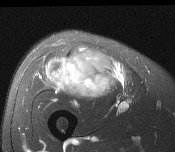
MRI of an extremity soft-tissue mass, one axial slice. Position 77 of 116 along the scan axis. T2-weighted fat-saturated. MR volume resampled by the dataset authors to the PET/CT grid (not the native acquisition matrix). 3.27 mm slice thickness. 175 × 152 image matrix, field of view 171 × 148 mm. Male patient. From the clinical record (not read from this slice): histological type: pleiomorphic leiomyosarcoma; grade: intermediate; site of the primary tumour: right thigh.
Outlined on this slice (expert contour drawn on MRI and transferred to this co-registered scan by the dataset authors):
- gross tumour volume including surrounding oedema: bounding box (x1, y1, x2, y2) in pixels: (47, 47, 114, 100)
- gross tumour volume (mass): (47, 49, 114, 100)